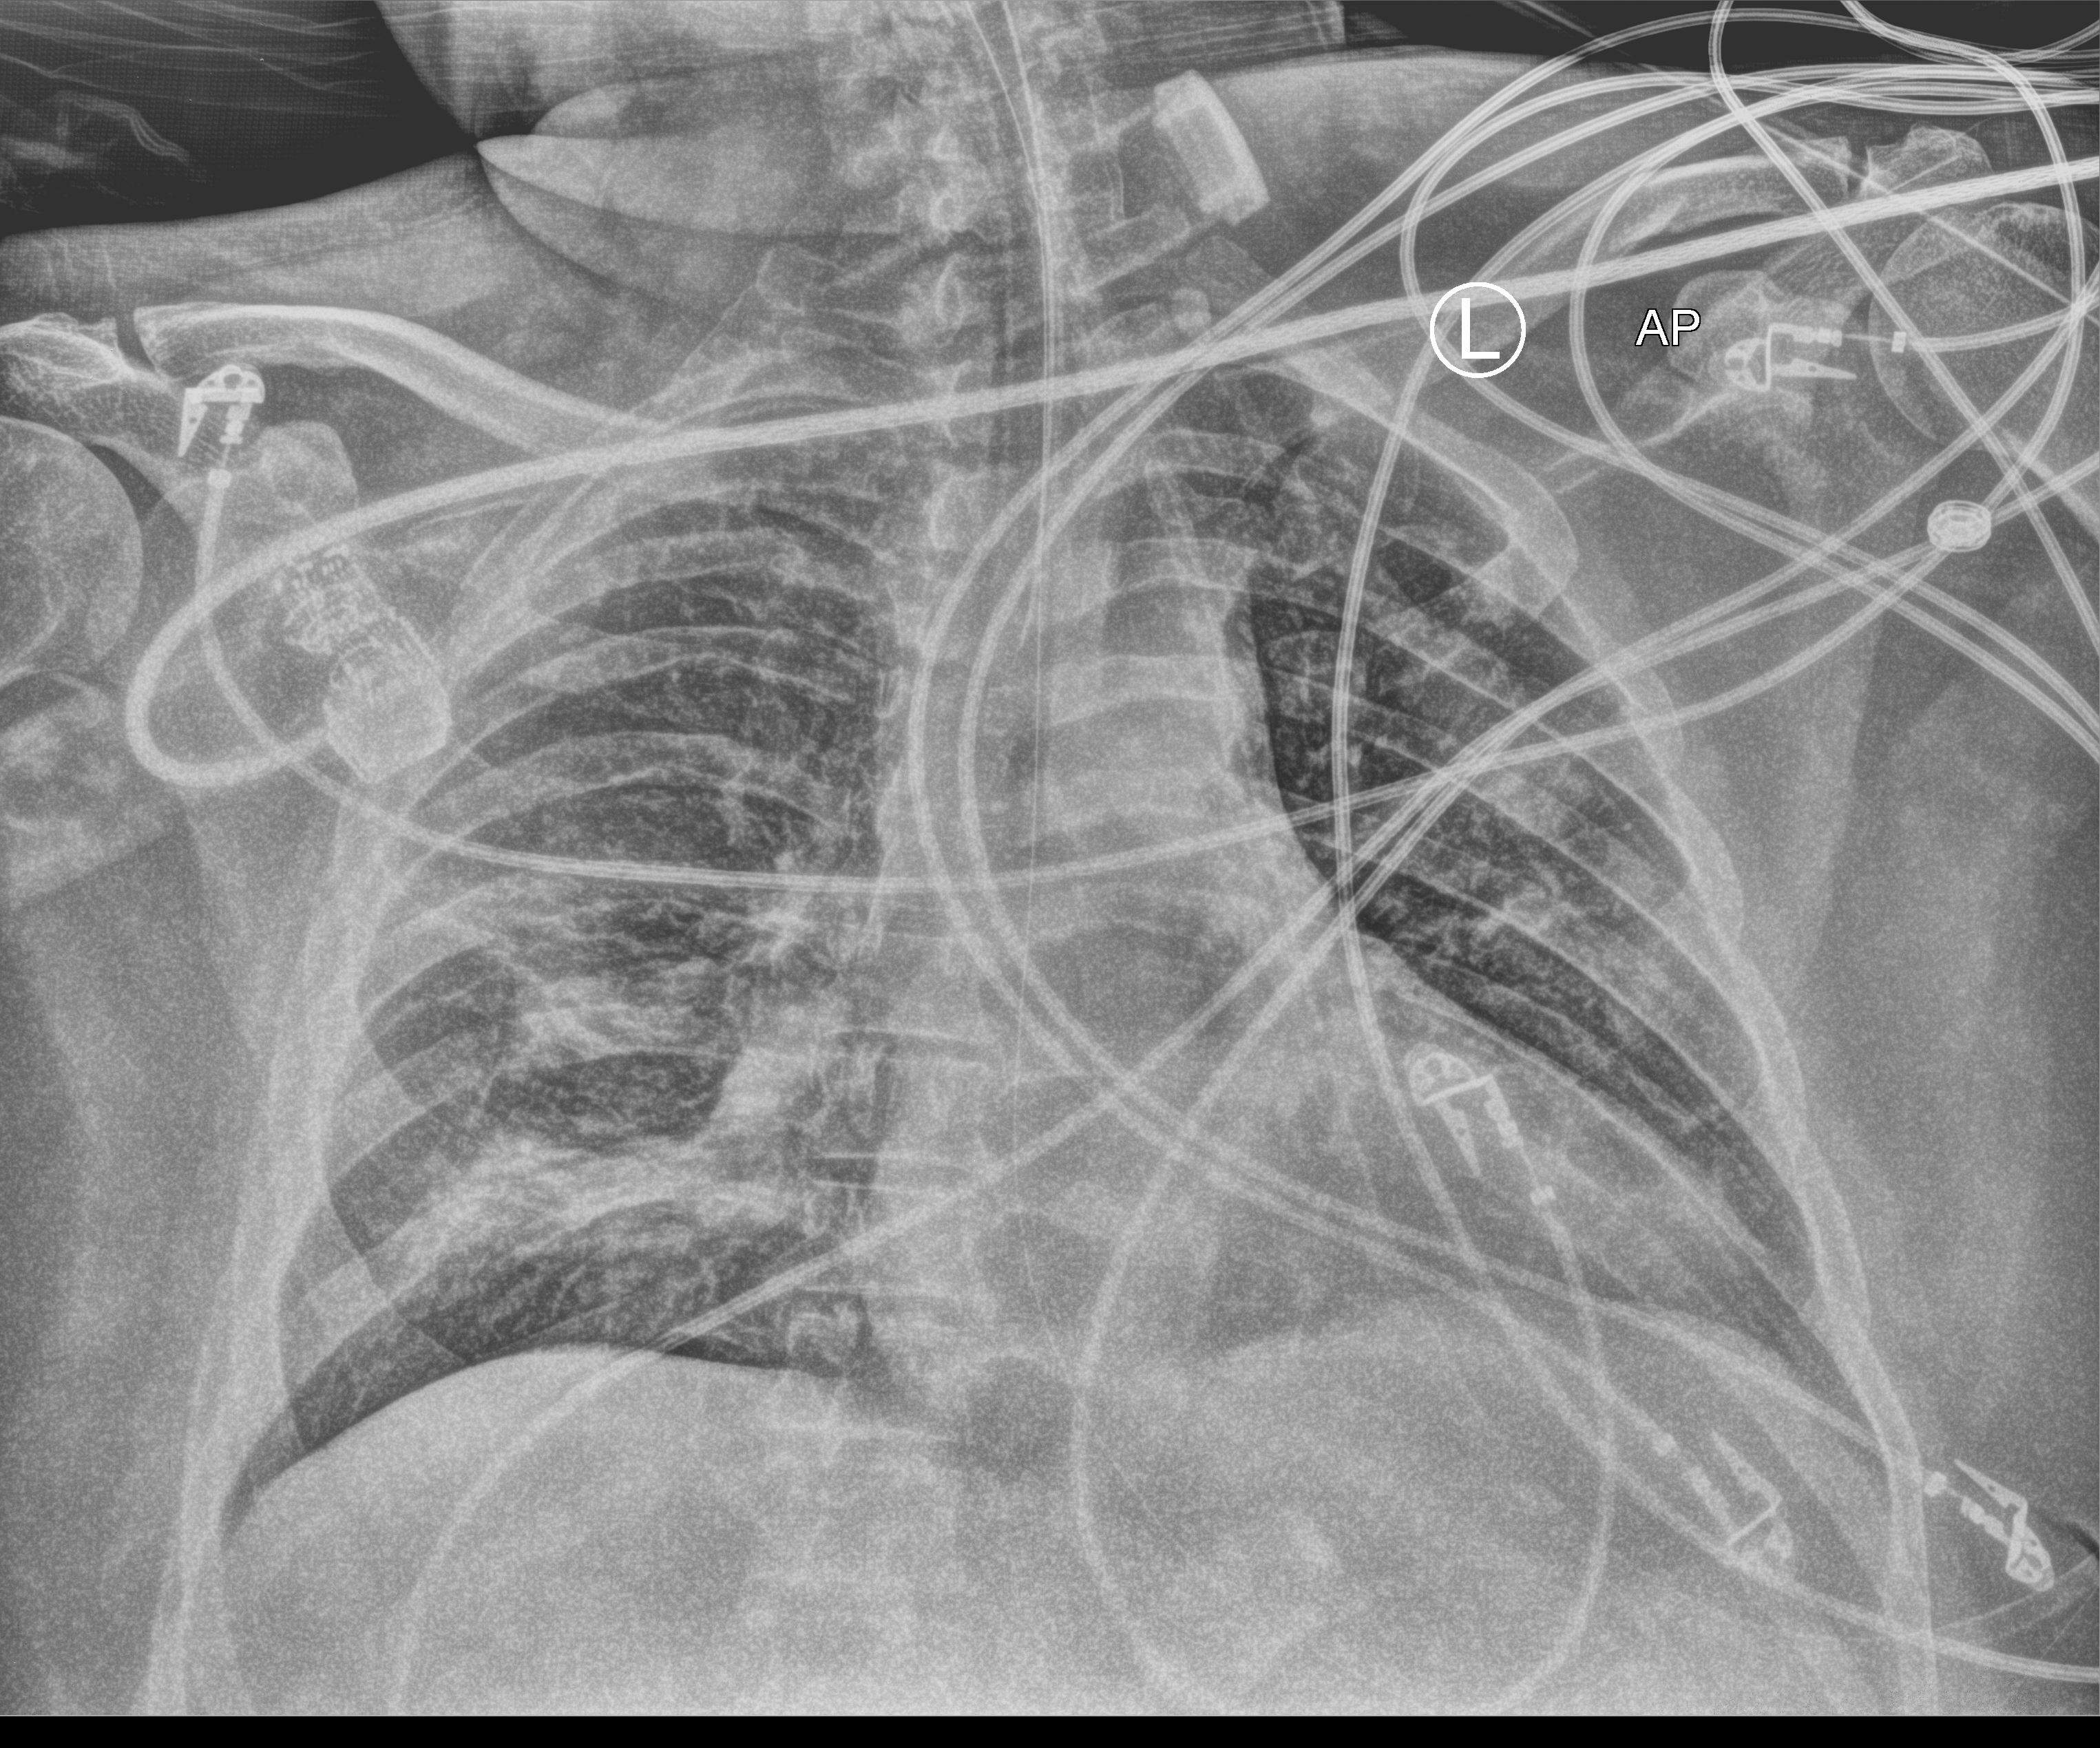
Portable chest radiograph, anteroposterior (AP) projection. Patient hospitalised with COVID-19; male, aged 60–74 years.
Hospital-stay facts (about this admission, not read from this image; timing relative to this image not recorded):
- mechanically ventilated during this hospital stay: yes
- diabetes (admission record): yes